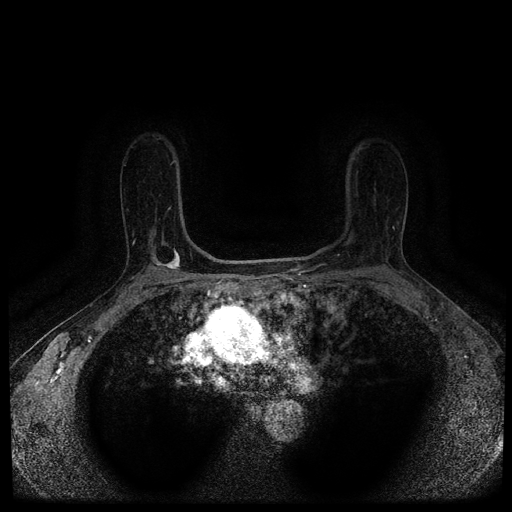
Breast MRI (dynamic contrast-enhanced, multi-phase), one axial slice. Position 72 of 116 along the scan axis. Dynamic contrast-enhanced series, time point 2 of 5 at this slice position (early post-contrast). 1.5 T. TE 2.7 ms, TR 5.4 ms. 2 mm slice thickness. 512 × 512 image matrix. Female patient, age 63 years.
Structures marked on this image (semi-automatically segmented with operator editing):
- breast lesion (labelled 'tumour' in the annotation; benign lesions carry a separate 'benign' label): box from (x=150, y=246) to (x=184, y=272) px